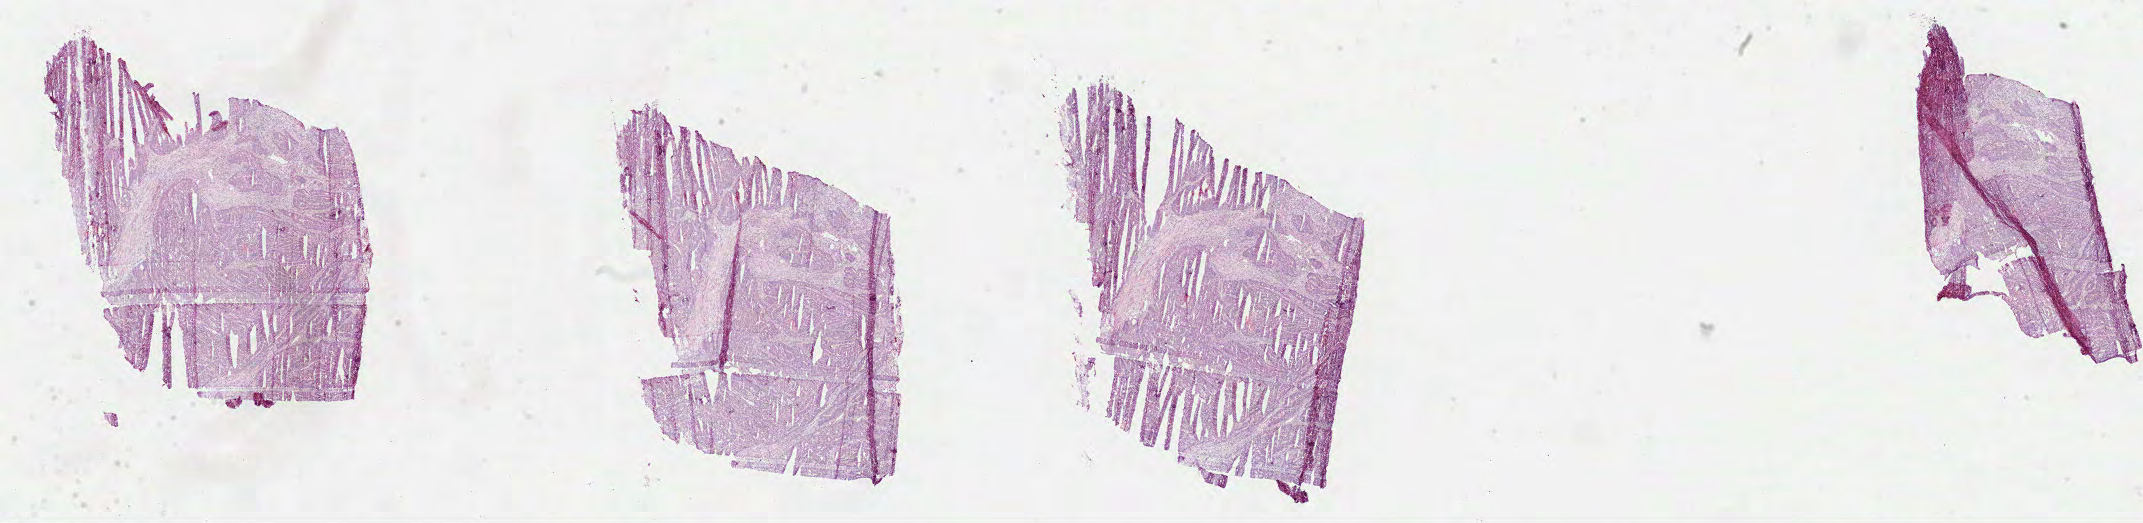
H&E-stained whole-slide image, whole scanned area (about 34.6 x 8.4 mm) shown as a low-resolution overview. Formalin-fixed paraffin-embedded (FFPE) diagnostic section. Sample: primary tumour, rectum. Female patient; age at initial diagnosis 57 years.
- AJCC pathologic stage: IV
- lymph nodes positive (case pathology): 2 of 13 examined
- histologic diagnosis: Tubular adenocarcinoma